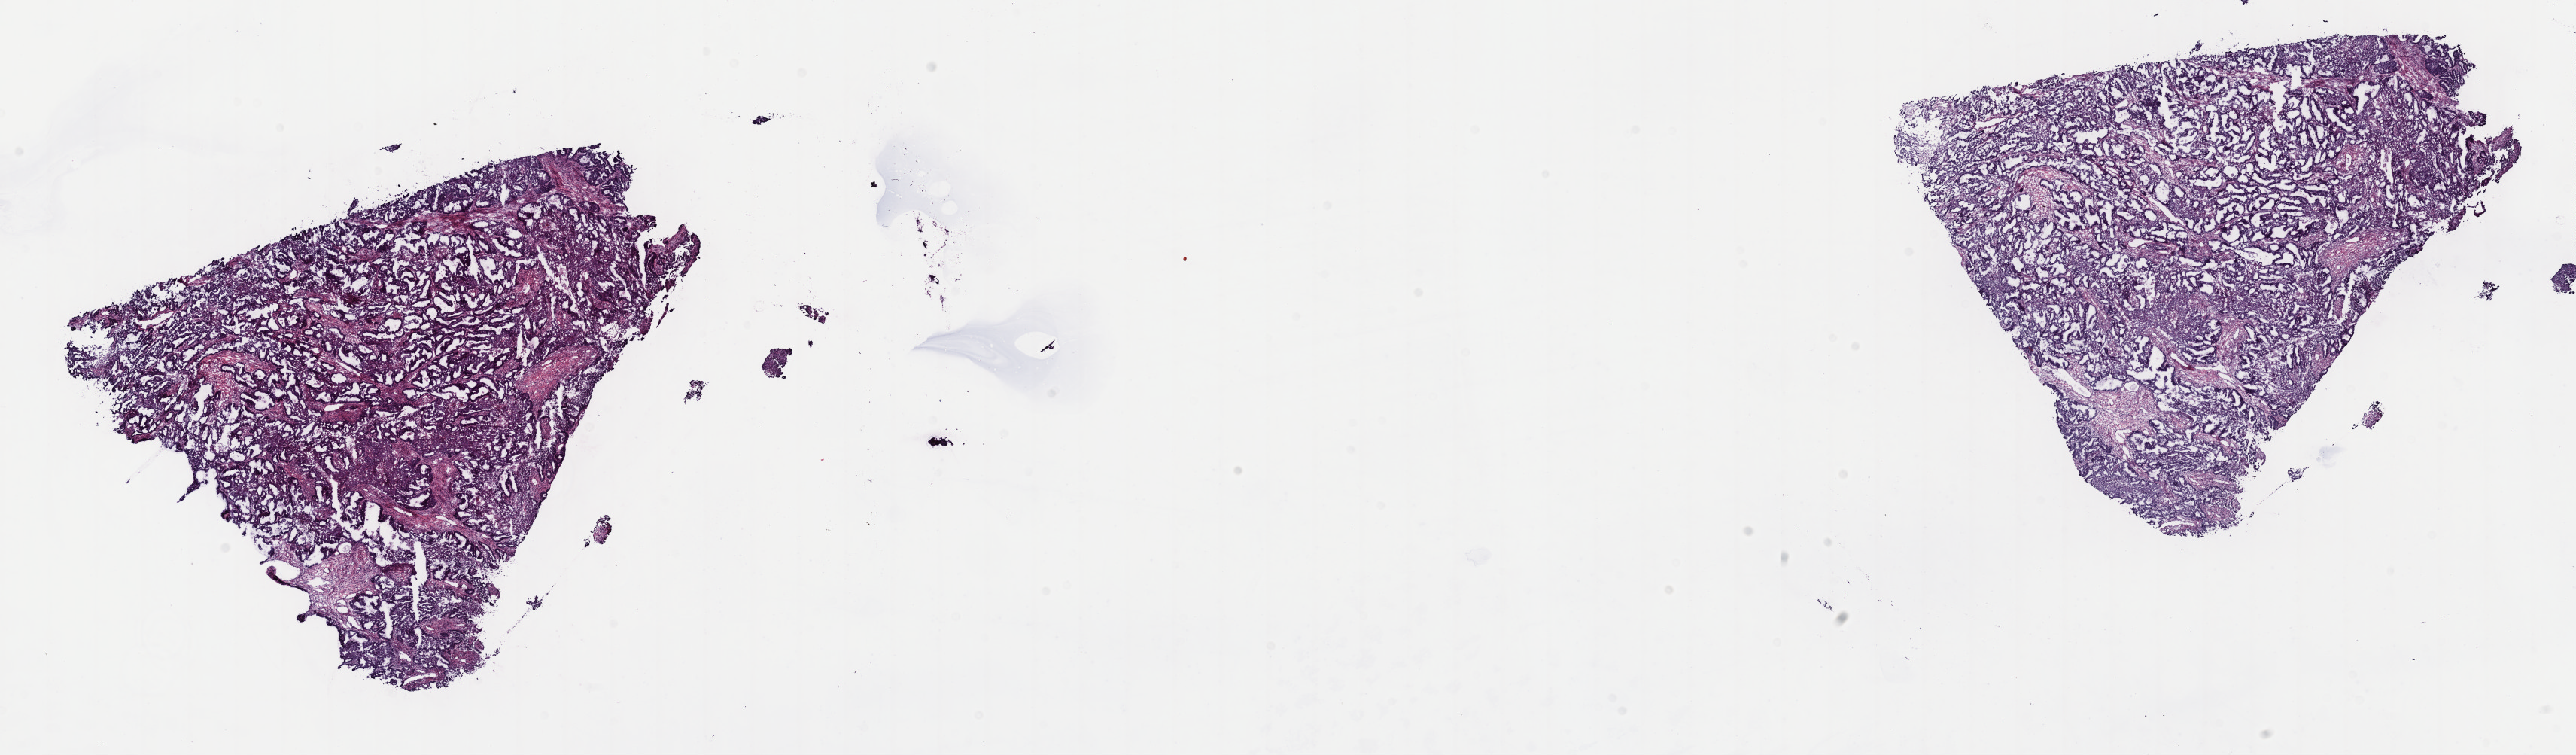
Whole-slide histology image, H&E-stained — shown as a low-resolution overview of the whole scanned area (about 27.7 x 8.1 mm, from a 40x scan), frozen section from the top of the tissue portion, uterus, primary tumour sample. Female patient; age at initial diagnosis 51 years. Histologic grade: G2 (moderately differentiated). Slide review estimates, as recorded: tumour cells 90%, tumour nuclei 90%, normal cells 2%, stromal cells 5%, necrosis 3%. Inflammatory infiltration, as recorded: lymphocyte infiltration 2%, monocyte infiltration 0%, neutrophil infiltration 0%.
Pathologic diagnosis: Endometrioid adenocarcinoma, NOS (endometrium). FIGO stage: IIIA. Lymph nodes positive (case pathology): 0 of 5 examined.